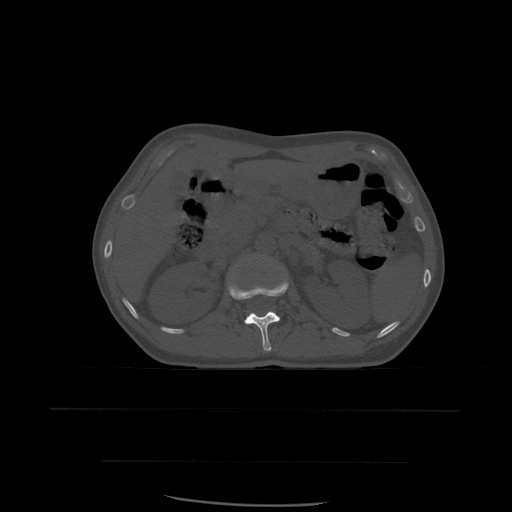
CT including the spine, one axial slice. Slice 244 of 574 in the series (ordered by position). Bone window (W 1800 / L 400 HU). 512 × 512 image matrix. Patient age 48 years. From the clinical record (not read from this slice): primary cancer: lung; vertebrae with lytic lesions (as recorded): T11.
Annotated regions visible in this slice (semi-automatic segmentation, software-assisted and operator-edited):
- L1 vertebra: box from (x=228, y=279) to (x=289, y=352) px